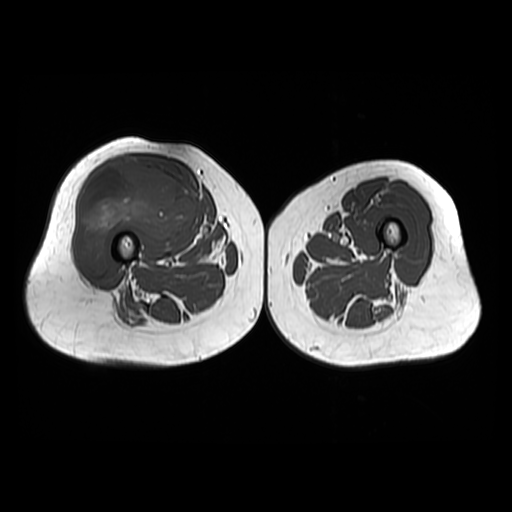
MRI of an extremity soft-tissue mass, one axial slice. Slice 27 of 48 in the series (ordered by position). 512 × 512 image matrix. Female patient. Case-level facts recorded for this patient, not image findings: histological type: pleiomorphic undifferentiated sarcoma; grade: high; site of the primary tumour: right quadricep.
Structures marked on this image (outlined manually by an expert reader):
- gross tumour volume including surrounding oedema: bounding box [x1, y1, x2, y2] px = [74, 156, 197, 275]
- gross tumour volume (mass): [74, 156, 197, 275]